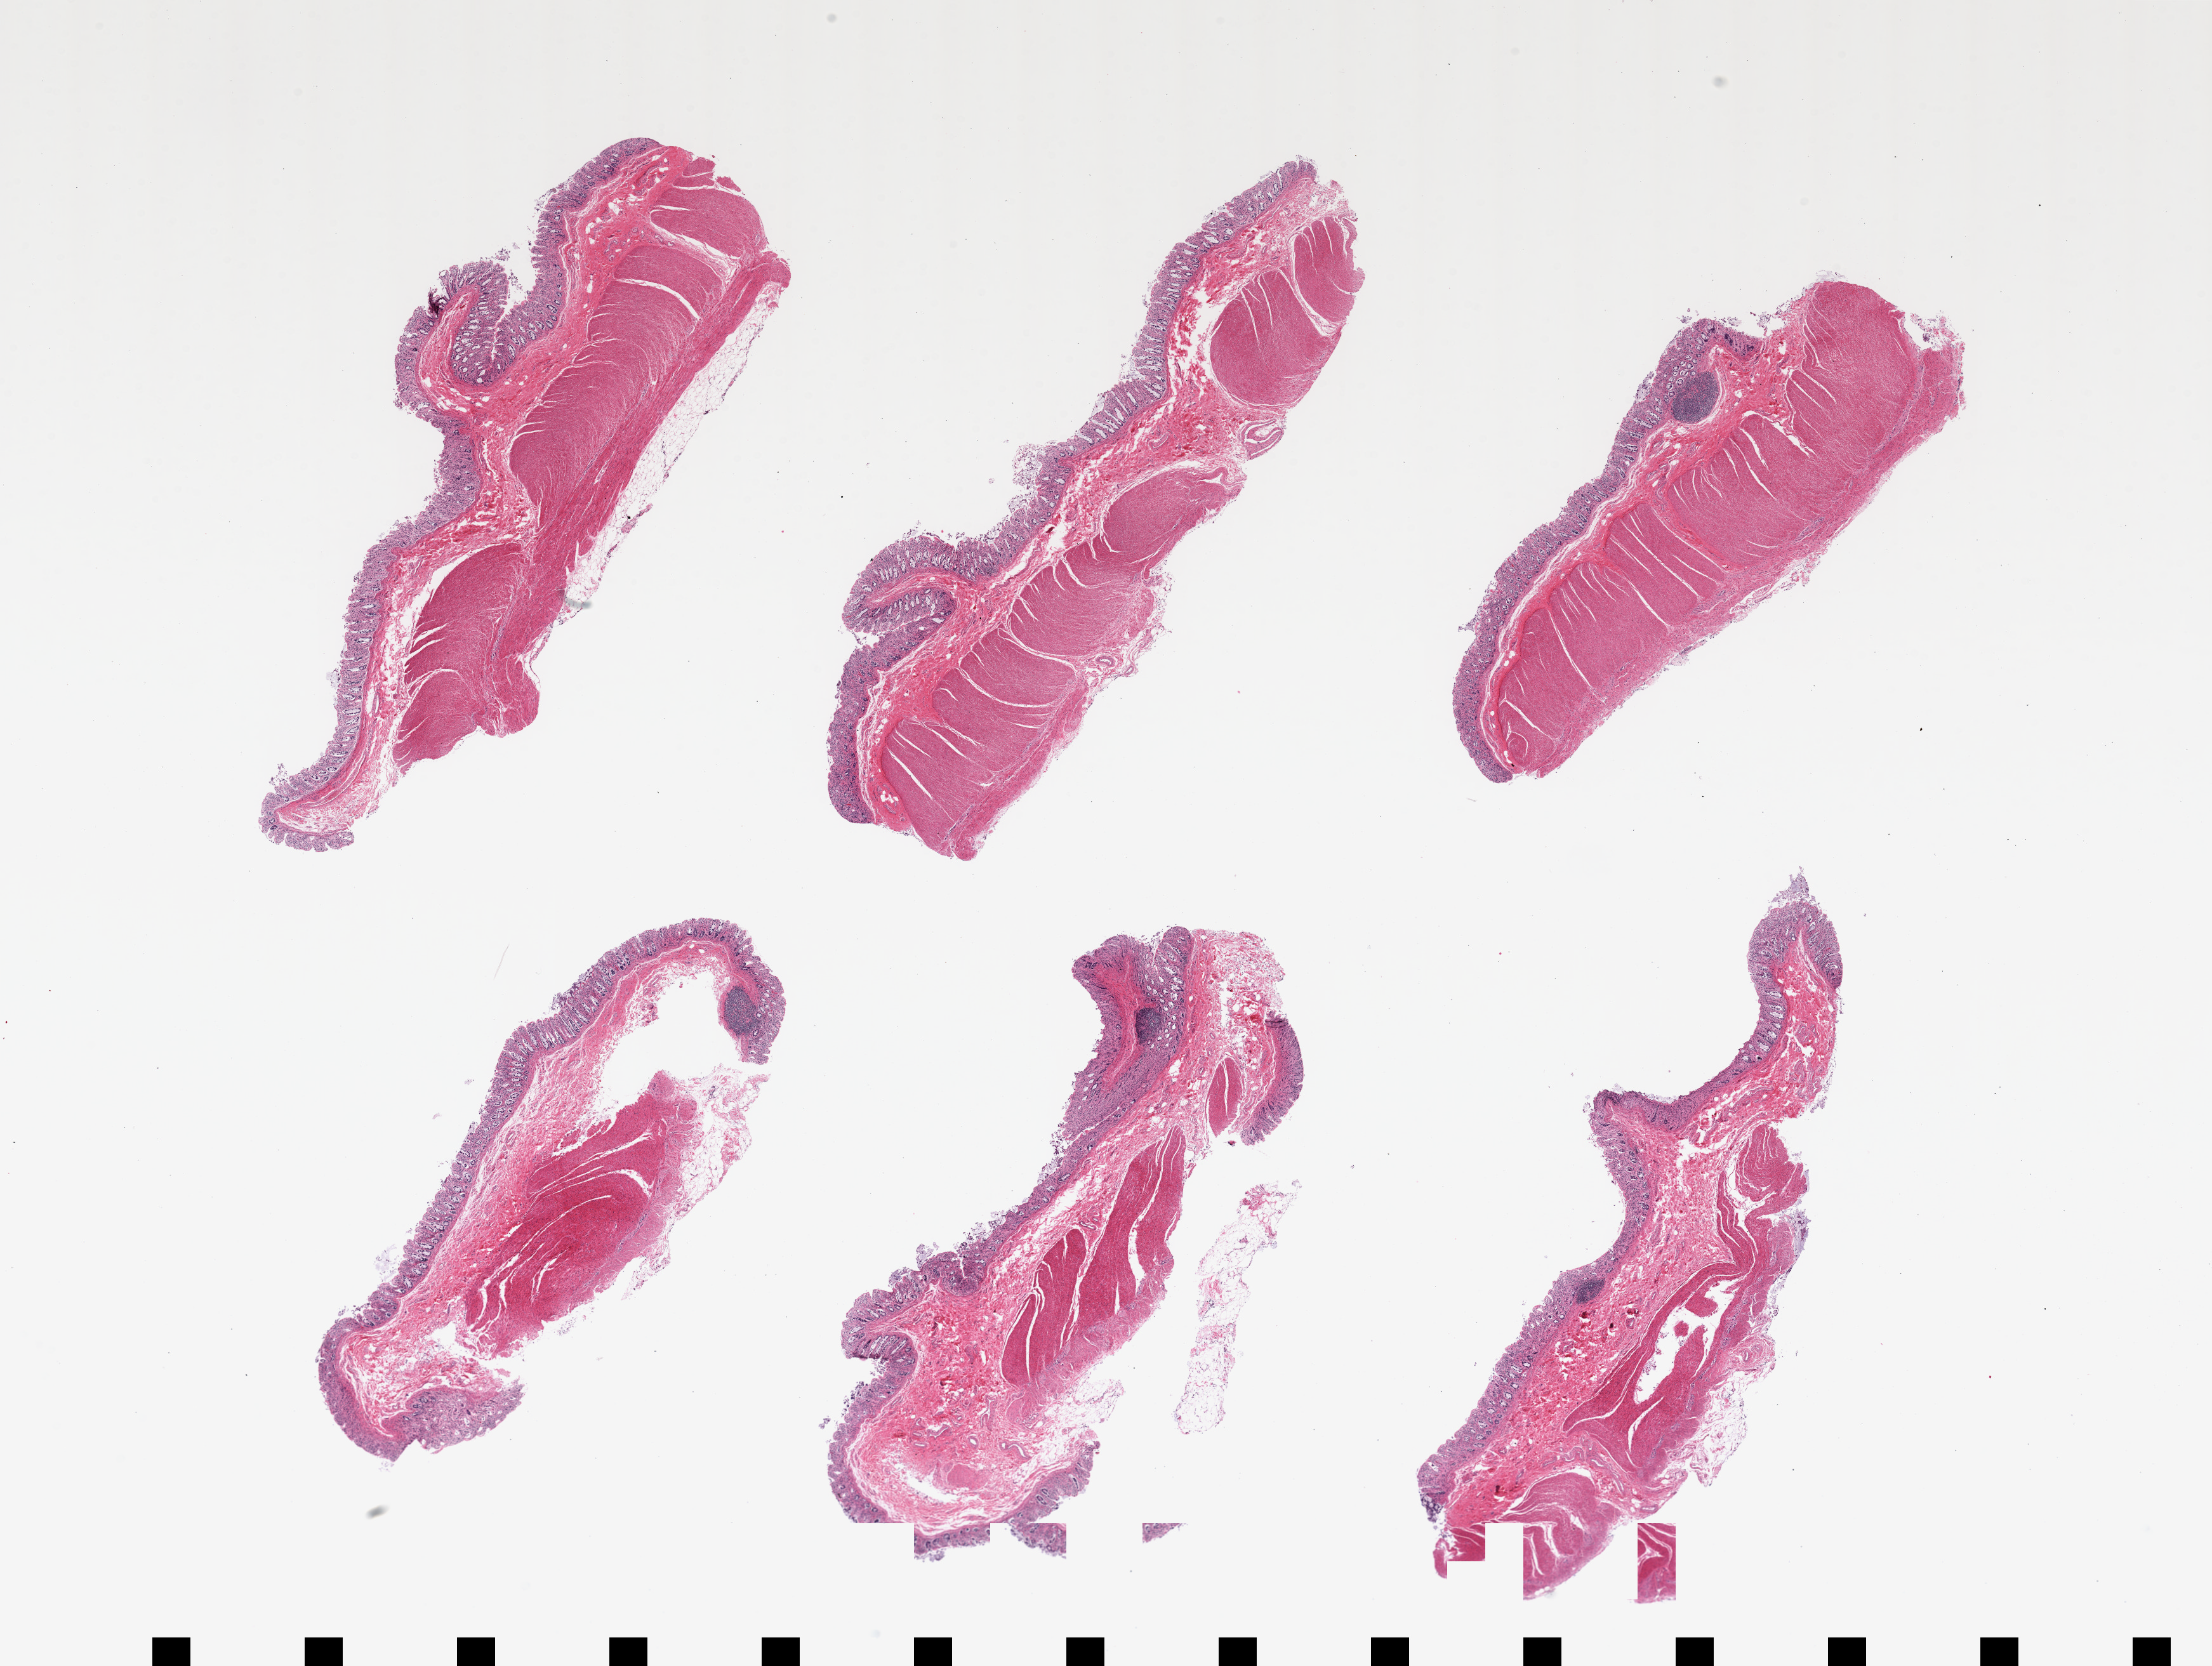
Whole-slide image, H&E stain — a low-resolution overview of the entire scanned area, about 27.6 x 20.8 mm; PAXgene-fixed, paraffin-embedded tissue; target tissue: sigmoid colon; tissue donor sample. Donor sex: male.
Pathologist's review note for this sample: 6 pieces, target muscularis is ~50-605 of tissue.